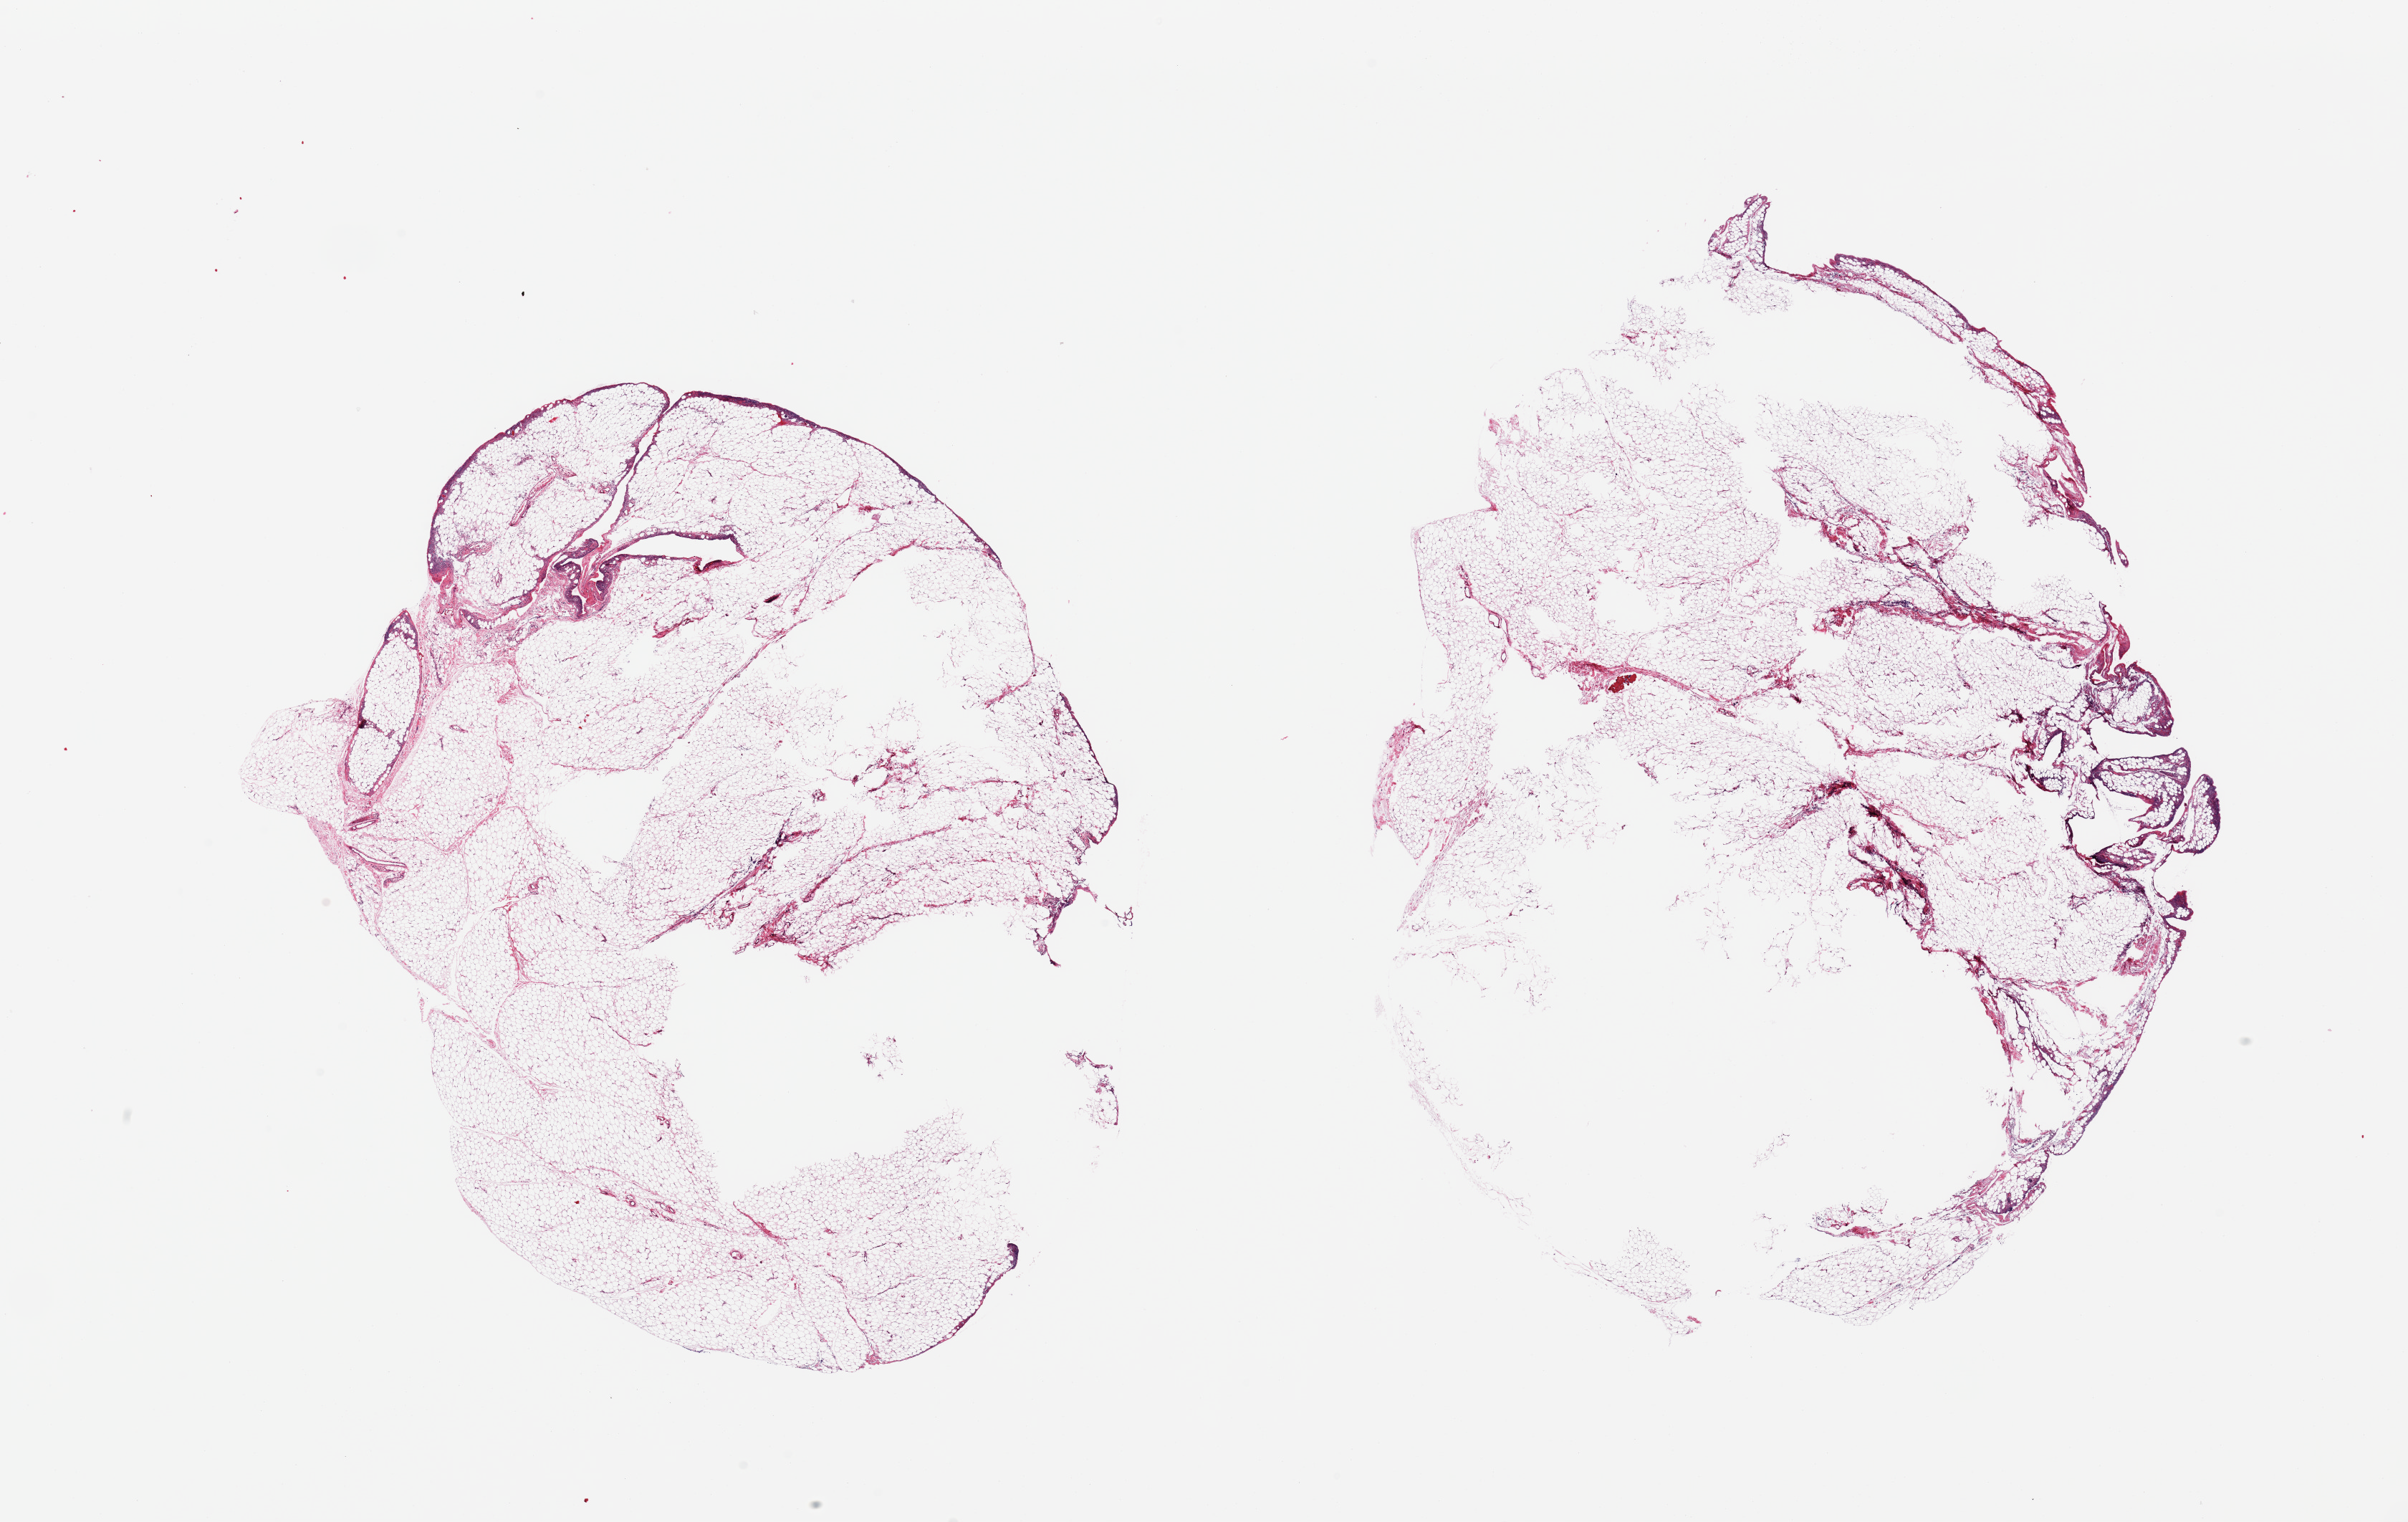
Digitized haematoxylin and eosin-stained section — low-resolution overview of the scanned area, about 26.6 x 16.8 mm (slide scanned at 20x). PAXgene-fixed, paraffin-embedded tissue. Target tissue: omentum. Tissue donor sample. Male donor.
• review note (as recorded): 2 pieces, <5% vascular/mesothelial elements